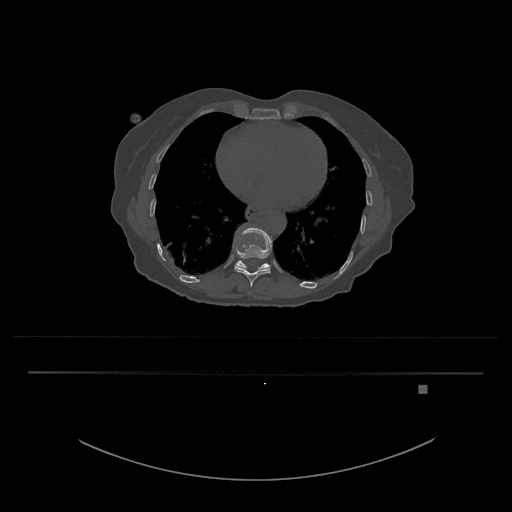
CT including the spine, one axial slice; position 700 of 797 along the scan axis; reconstruction kernel Br40s/3; 120 kVp; bone window (W 1800 / L 400 HU); 0.5 mm slice thickness; 512 × 512 image matrix, field of view 500 × 500 mm. Female patient, age 57 years. Case-level facts recorded for this patient, not image findings: primary cancer: cervical.
Structures marked on this image (semi-automatically segmented with operator editing):
- T10 vertebra: bounding box [x1, y1, x2, y2] px = [233, 227, 272, 287]
- T11 vertebra: [235, 258, 271, 270]